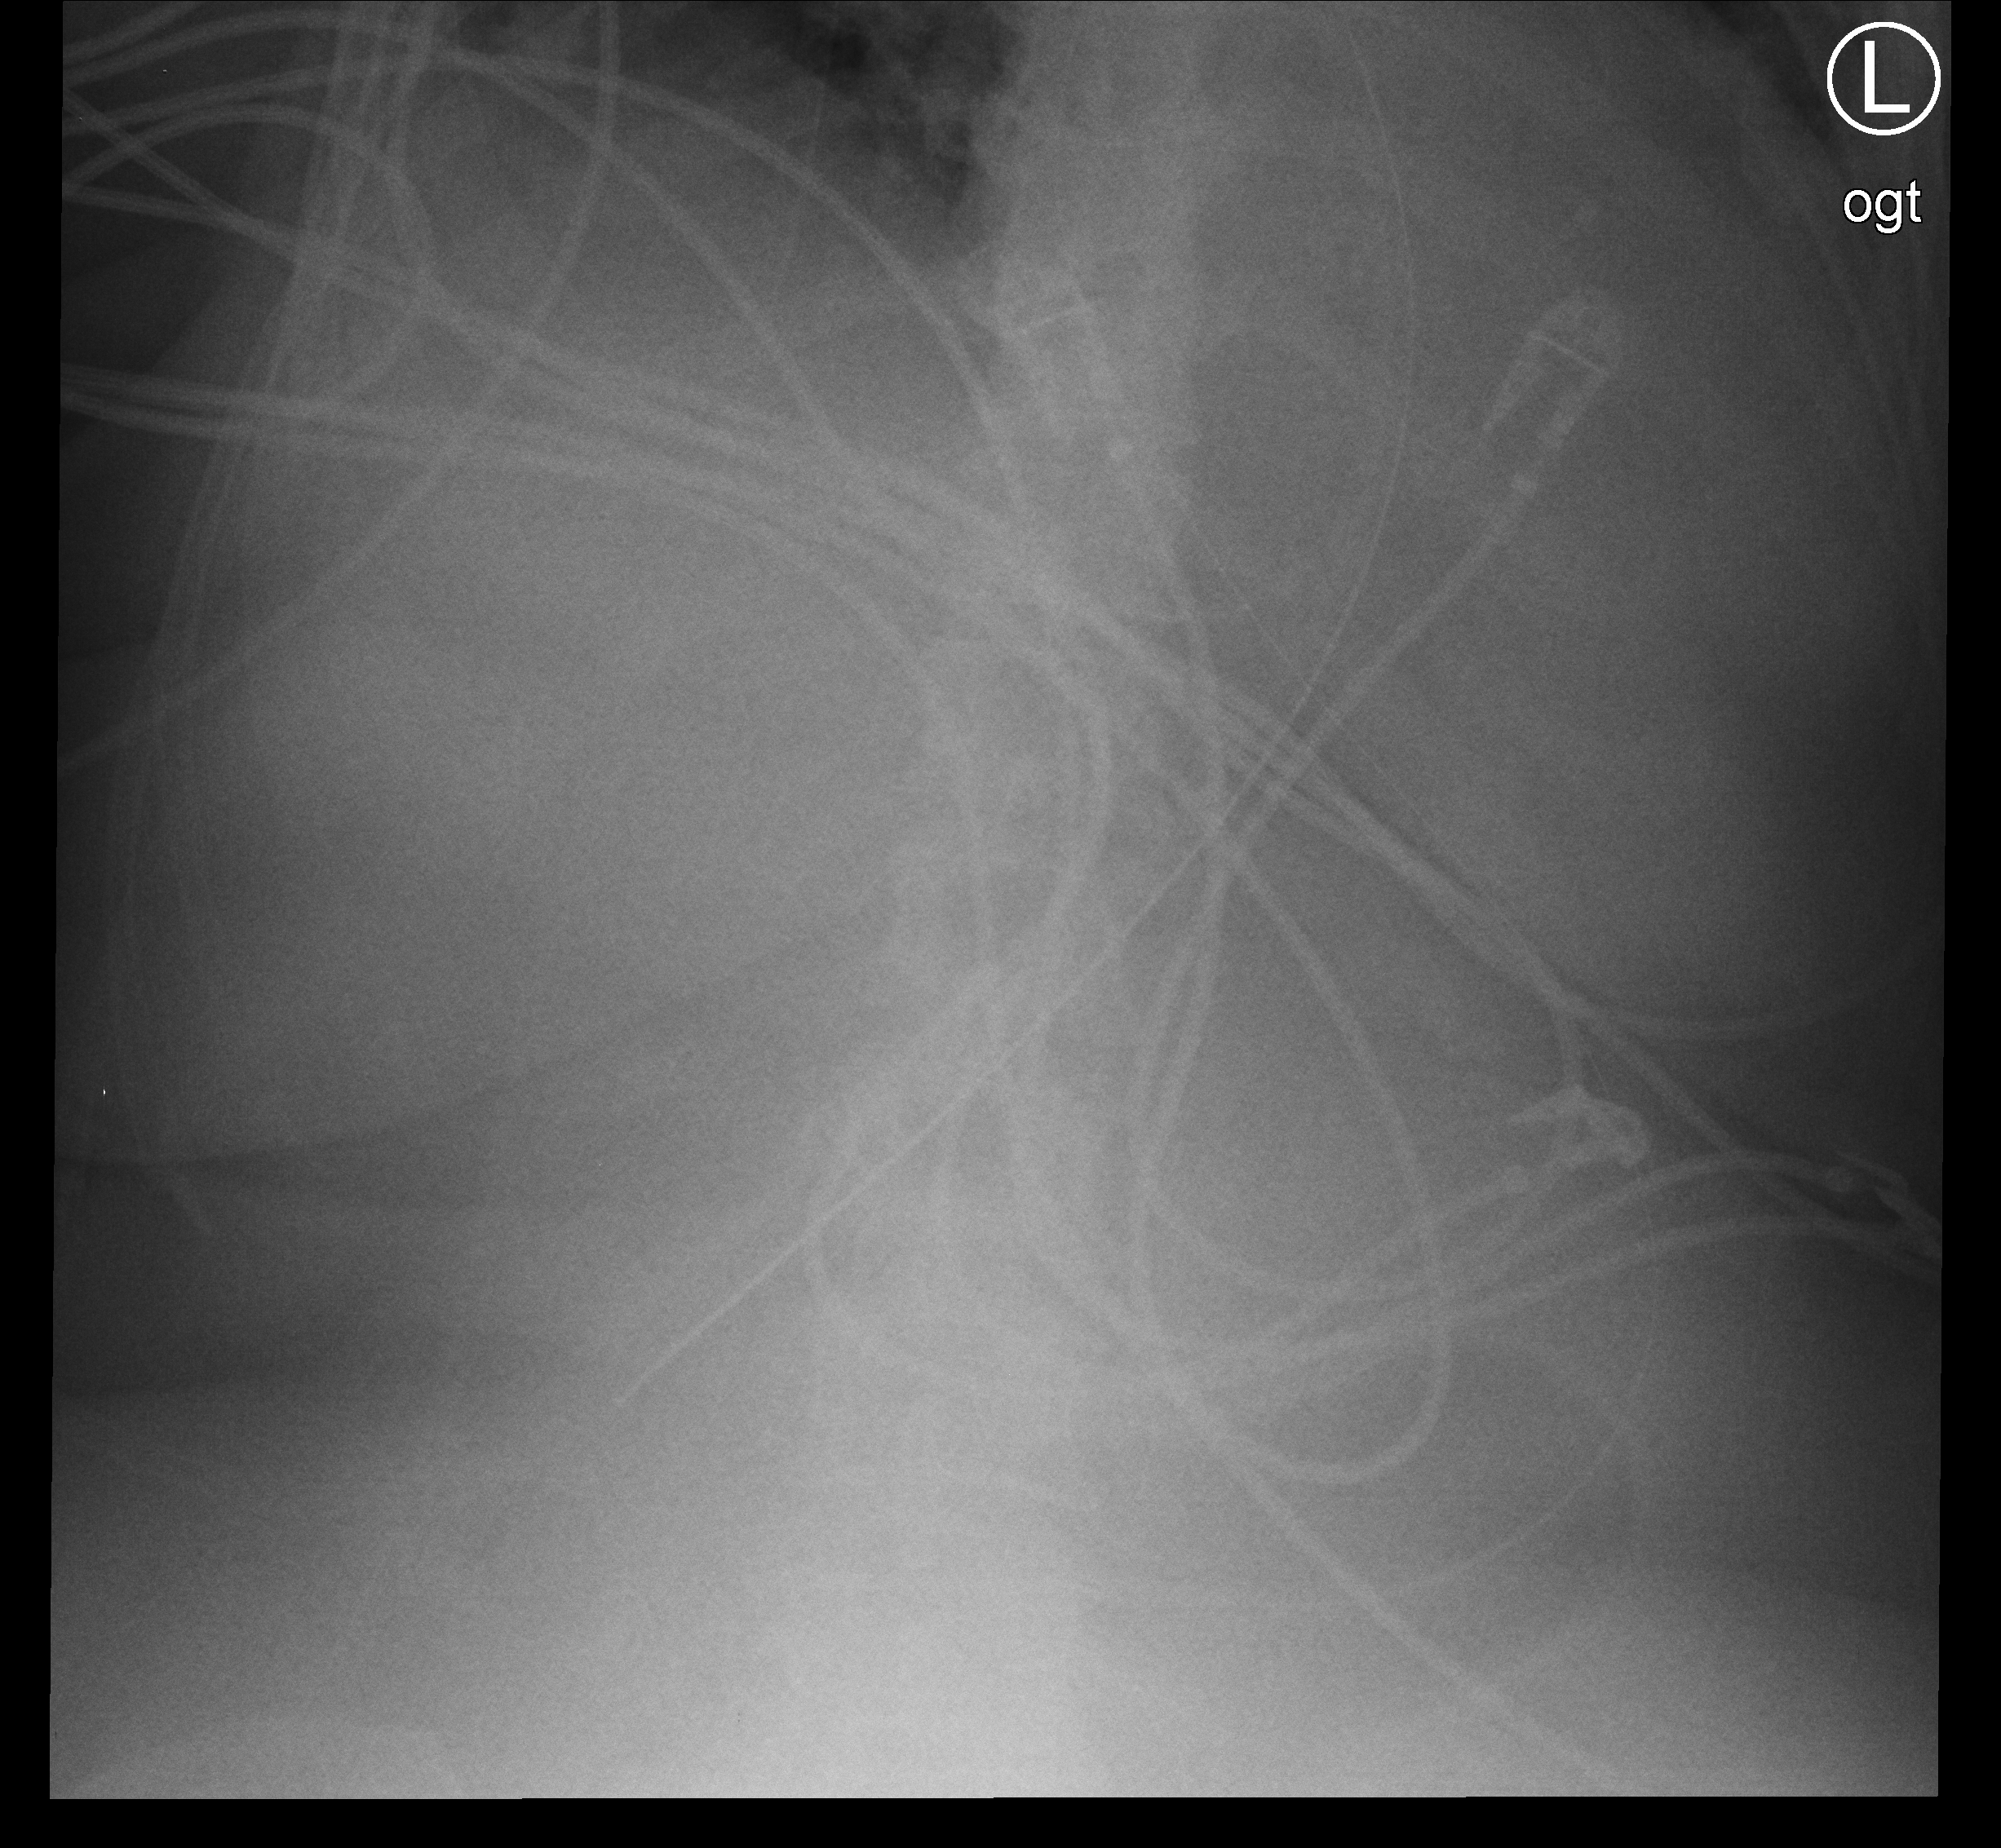
Portable chest radiograph, anteroposterior (AP) projection. Patient hospitalised with COVID-19; female, aged 60–74 years.
Hospital-stay facts (about this admission, not read from this image; timing relative to this image not recorded): admitted to intensive care during this hospital stay: yes; length of hospital stay: 50 days.